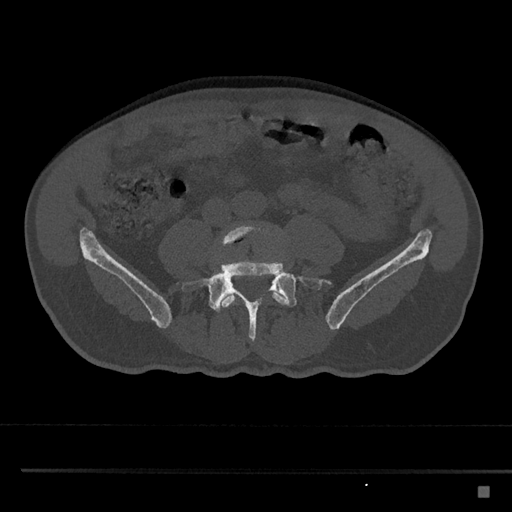
CT including the spine, one axial slice. Position 601 of 797 along the scan axis. 120 kVp. Bone window (W 1800 / L 400 HU). 512 × 512 image matrix, field of view 391 × 391 mm. Patient: male, 59 years. Case-level facts recorded for this patient, not image findings: primary cancer: prostate.
Annotated regions visible in this slice (semi-automatically segmented with operator editing):
- L4 vertebra: box from (x=216, y=223) to (x=289, y=312) px
- L5 vertebra: (x=179, y=253)–(x=330, y=342)